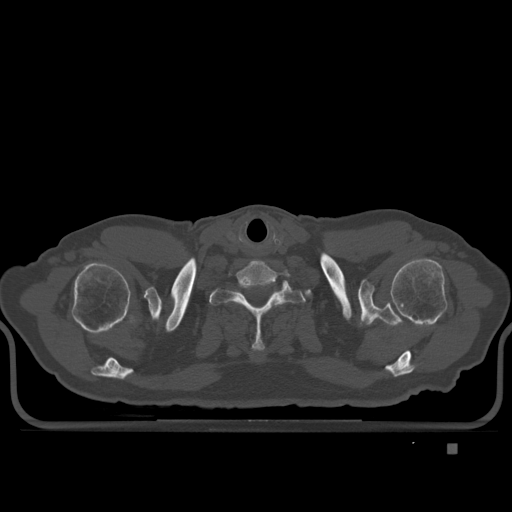
CT including the spine, one axial slice. Position 328 of 435 along the scan axis. Bone window (W 1800 / L 400 HU). 512 × 512 image matrix. Male patient, age 73 years. Case-level facts recorded for this patient, not image findings: primary cancer: skin.
Annotated regions visible in this slice (semi-automatic segmentation, software-assisted and operator-edited):
- T1 vertebra: bounding box (x1, y1, x2, y2) in pixels: (209, 282, 305, 352)